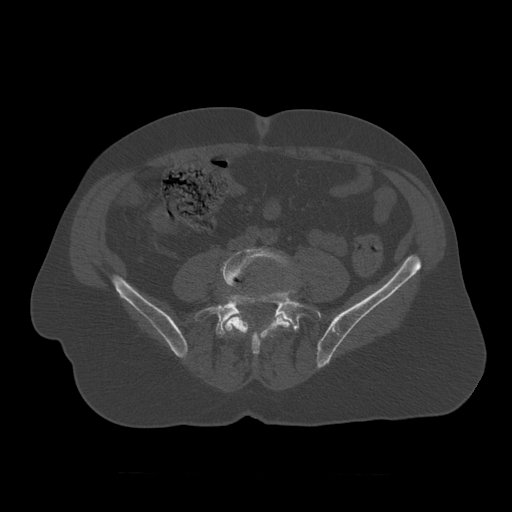
CT including the spine, one axial slice. Slice 264 of 450 in the series (ordered by position). Reconstruction kernel STANDARD. 120 kVp. Bone window (W 1800 / L 400 HU). 512 × 512 image matrix. Patient age 75 years. Case-level facts recorded for this patient, not image findings: primary cancer: prostate.
Structures marked on this image (semi-automatic segmentation, software-assisted and operator-edited):
- L4 vertebra: bounding box (x1, y1, x2, y2) in pixels: (221, 248, 298, 357)
- L5 vertebra: (195, 290, 323, 338)